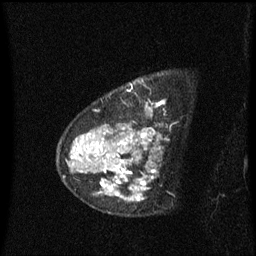
Breast MRI (dynamic contrast-enhanced), one sagittal slice. Position 46 of 60 along the scan axis. Dynamic contrast-enhanced series, image 2 of 3 at this slice position (ordered by acquisition). 1.5 T. TE 4.2 ms, TR 8.4 ms. 2 mm slice thickness. 256 × 256 image matrix, field of view 200 × 200 mm. Patient: female, 48 years. Case-level facts recorded for this patient, not image findings: setting: breast cancer imaged before/during neoadjuvant chemotherapy; receptor status: HR-positive, HER2-negative.
Annotated regions visible in this slice (semi-automatic segmentation, software-assisted and operator-edited):
- analysis volume of interest (the breast-tissue region the enhancement analysis was run in; not a lesion): box from (x=80, y=80) to (x=167, y=215) px
- tumour enhancement mask (voxels above the 70 % enhancement threshold inside the analysis volume of interest): (x=80, y=104)–(x=159, y=202)